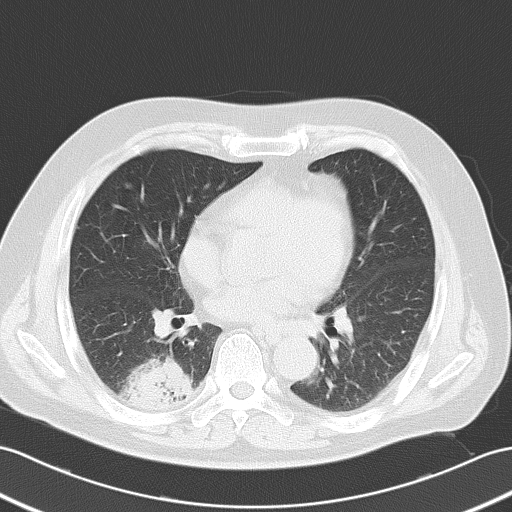
Chest CT, one axial slice. Slice 19 of 52 in the series (ordered by position). Reconstruction kernel B70f. 120 kVp. Lung window (W 1500 / L -600 HU). 5 mm slice thickness. 512 × 512 image matrix, field of view 353 × 353 mm. Male patient, age 70 years. From the clinical record (not read from this slice): clinical TNM (as recorded): T2 N0 M0; histopathological grade: G2.
Annotated regions visible in this slice (bounding box drawn by a radiologist):
- lung tumour (recorded histology: adenocarcinoma): box from (x=122, y=353) to (x=198, y=416) px